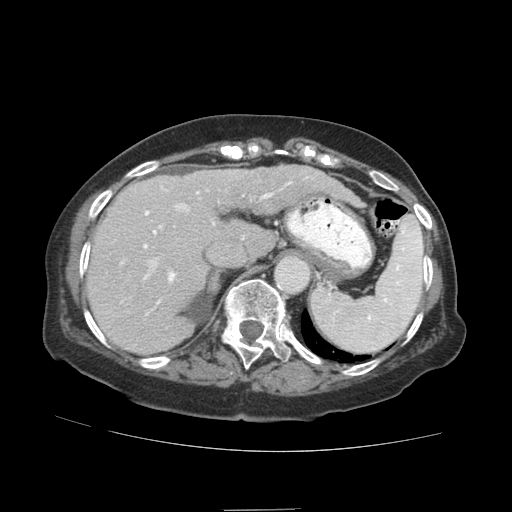
Contrast-enhanced abdominal CT (liver protocol), one axial slice; slice 64 of 89 in the series (ordered by position); soft-tissue window (W 400 / L 40 HU); 2.5 mm slice thickness; 512 × 512 image matrix, field of view 360 × 360 mm. Case-level facts recorded for this patient, not image findings: diagnosis: hepatocellular carcinoma (patient treated with transarterial chemoembolisation; whether this scan precedes or follows treatment is not stated here); TNM stage (as recorded): Stage-II; Child-Pugh class: A; tumour nodularity: multinodular; tumour size: 4 cm.
Structures marked on this image (semi-automatic segmentation, software-assisted and operator-edited):
- liver parenchyma outside the tumour (the mass and vessels are separate outlines, so this box may not span the whole liver): box from (x=86, y=166) to (x=296, y=353) px
- liver vessels: (x=119, y=171)–(x=287, y=316)